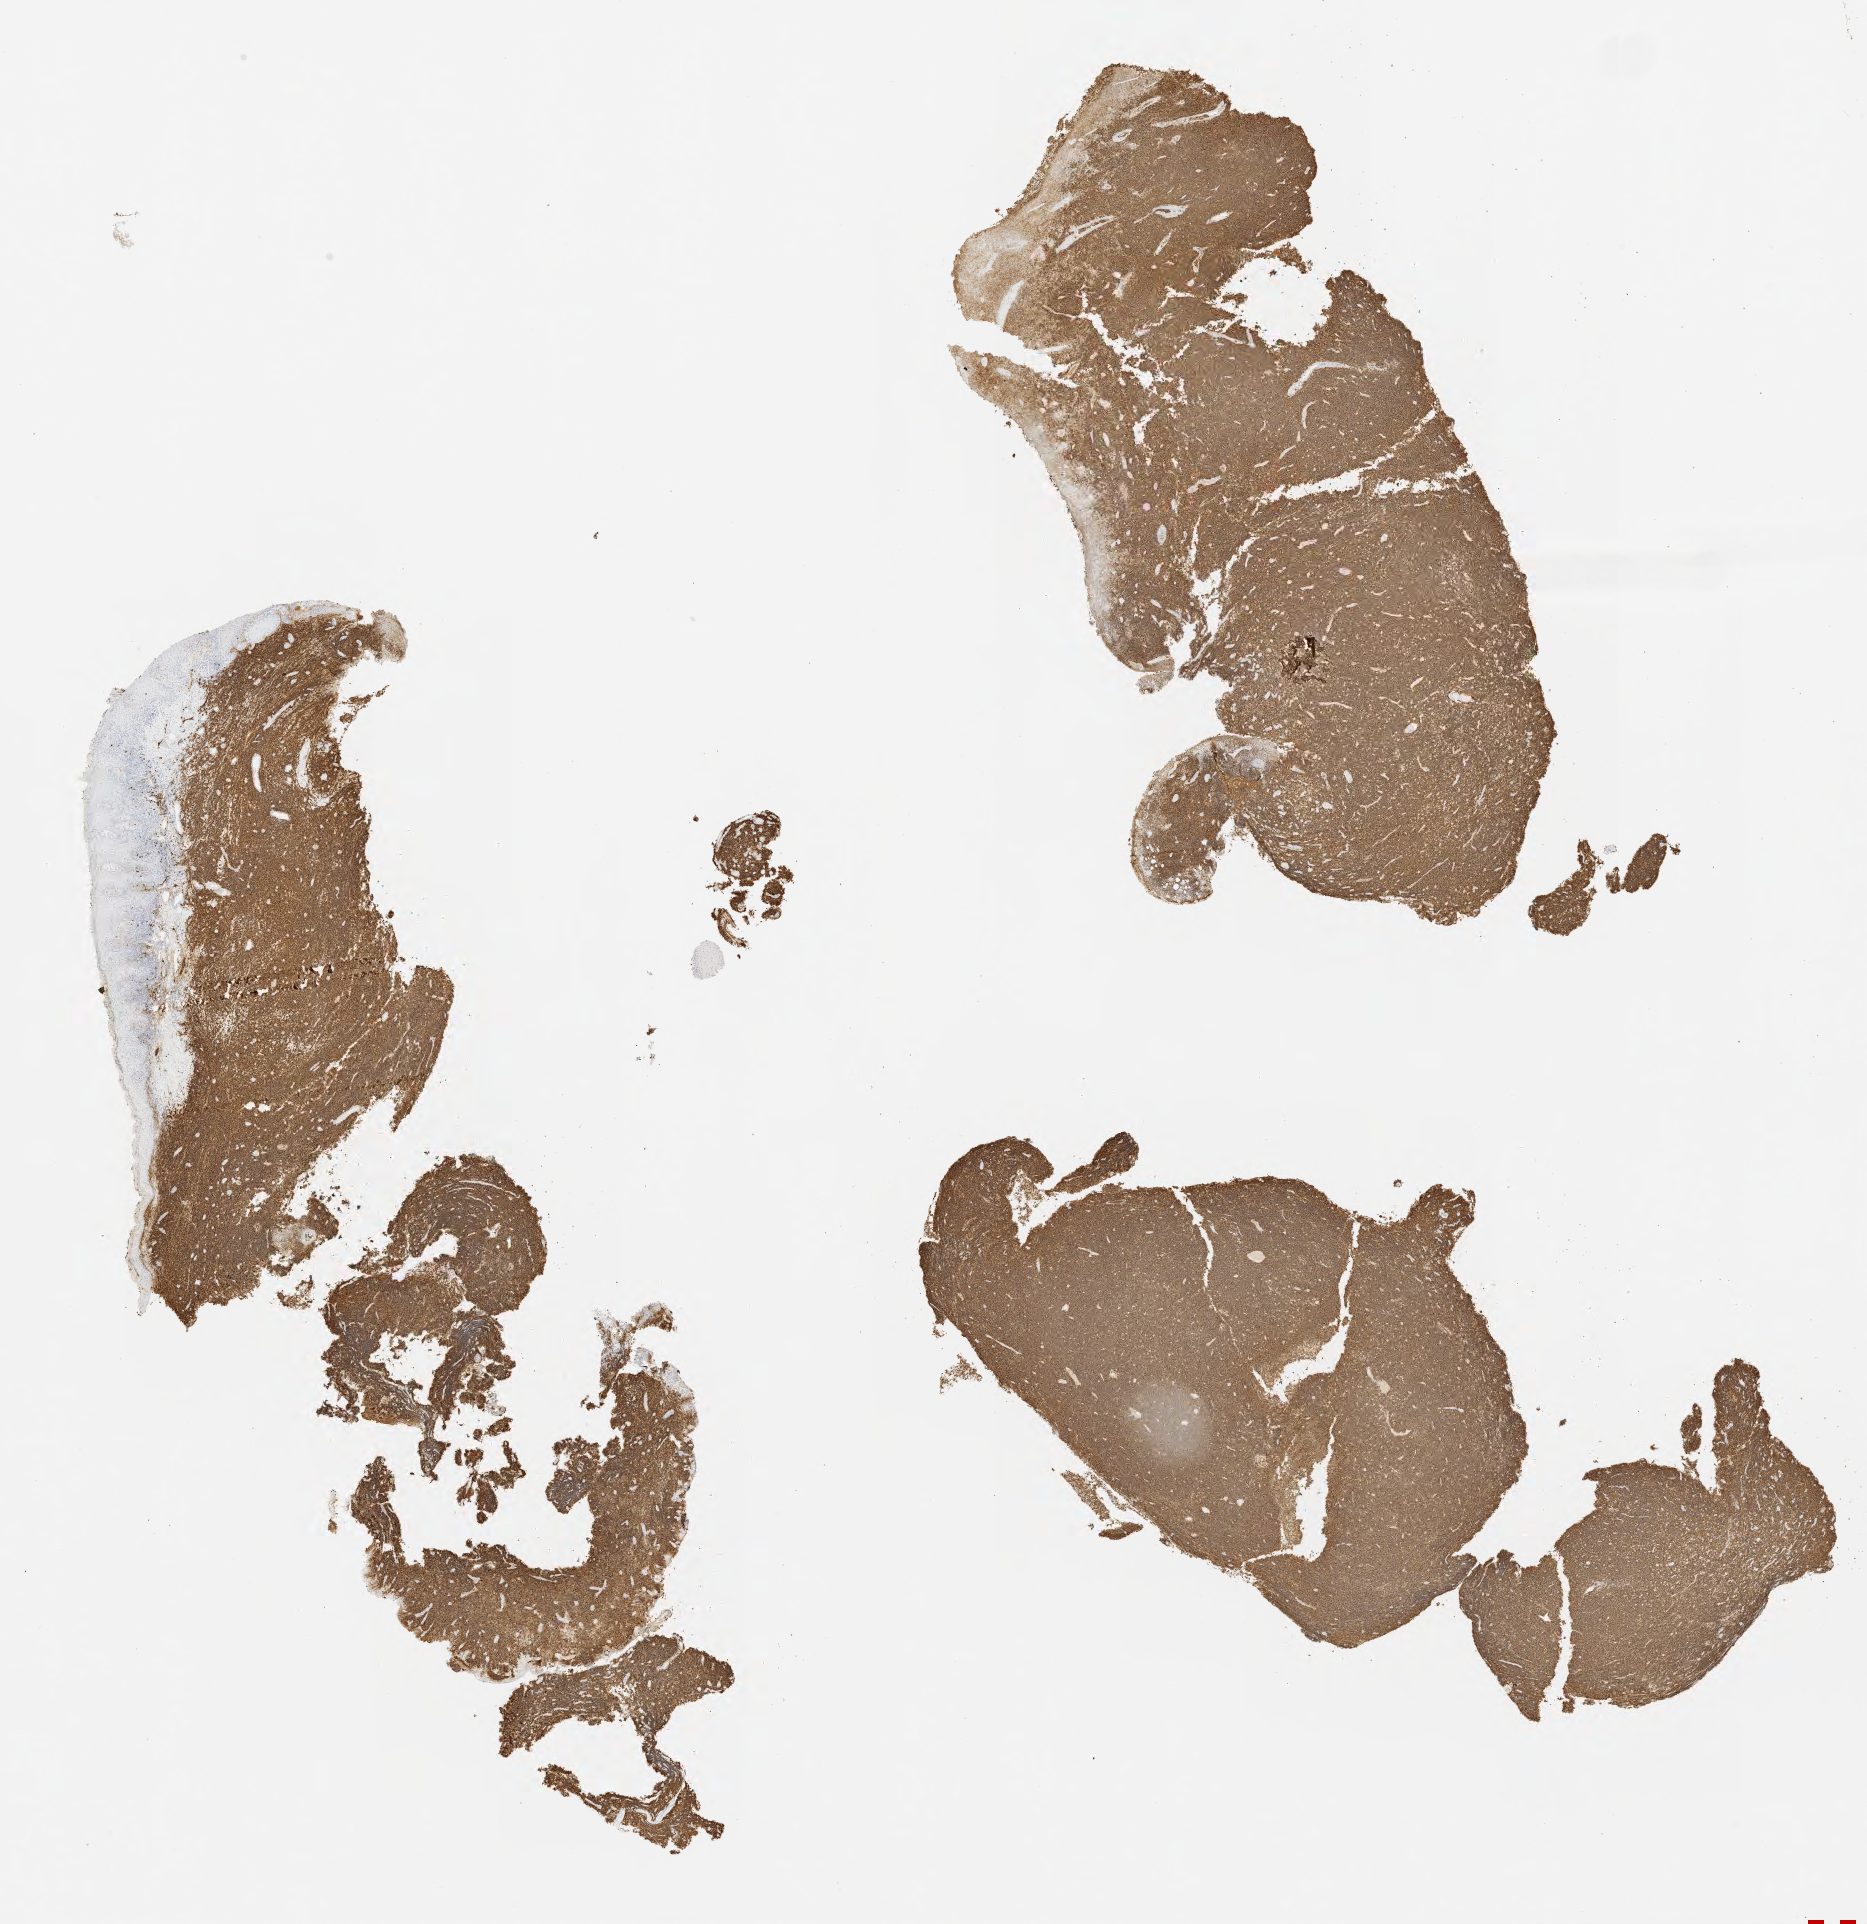
Immunohistochemistry (IHC) whole-slide image stained for CD20, low-resolution overview of the scanned area, about 15.0 x 15.5 mm, specimen: tumor tissue. Patient: male, age 22 years.
- histologic diagnosis: Burkitt lymphoma, NOS